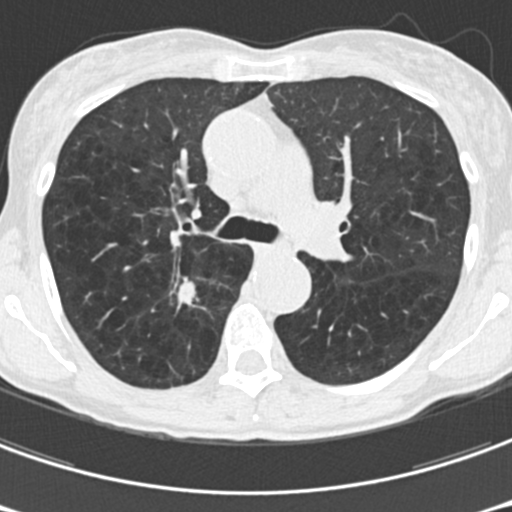
Axial slice from a low-dose chest CT screening exam. Third screening round (two years after baseline). Lung window (W 1500 / L -600 HU). 2 mm slice thickness. Standard (soft-tissue) reconstruction kernel (B30f). 120 kVp. 512 × 512 image matrix, field of view 277 × 277 mm. Female participant, aged 61 years at enrolment.
Expert reader's lesion annotation, bounding box [x1, y1, x2, y2] px = [162, 265, 225, 325]. The screening reader recorded 2 non-calcified nodules or masses ≥4 mm on this exam (right upper lobe, right upper lobe); which of them this box marks is not recorded. Official screen result: positive, other.